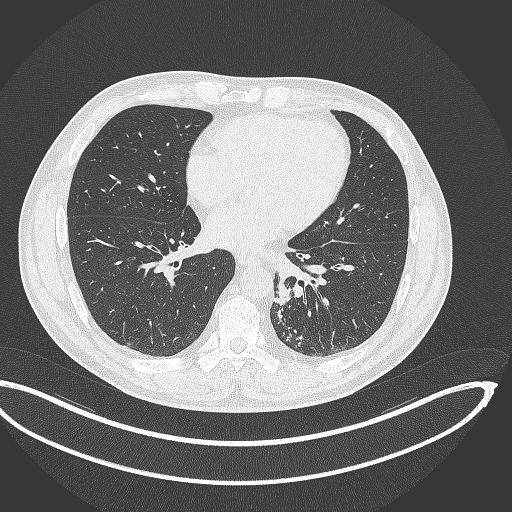
Chest CT, one axial slice. Position 142 of 362 along the scan axis. Lung window (W 1500 / L -600 HU). 512 × 512 image matrix, field of view 442 × 442 mm. Patient: male, 50 years. From the clinical record (not read from this slice): clinical TNM (as recorded): T2a N3 M0.
Structures marked on this image (bounding box drawn by a radiologist):
- lung tumour (recorded histology: squamous cell carcinoma): bounding box <271,280,294,305> (left, top, right, bottom; pixels)